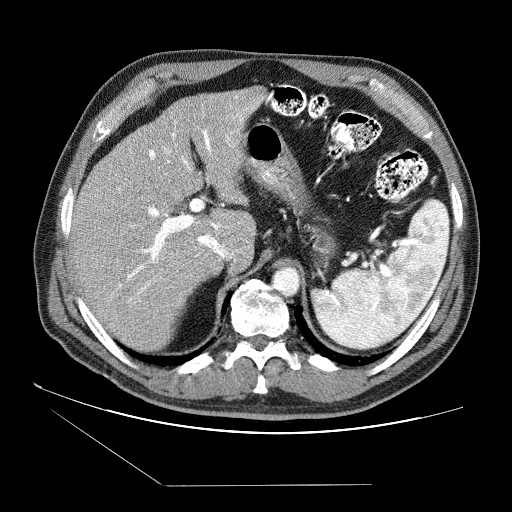
Contrast-enhanced abdominal CT (liver protocol), one axial slice. Slice 54 of 87 in the series (ordered by position). Reconstruction kernel STANDARD. Soft-tissue window (W 400 / L 40 HU). 2.5 mm slice thickness. 512 × 512 image matrix, field of view 400 × 400 mm. From the clinical record (not read from this slice): diagnosis: hepatocellular carcinoma (patient treated with transarterial chemoembolisation; whether this scan precedes or follows treatment is not stated here); TNM stage (as recorded): Stage-II; Child-Pugh class: B; tumour nodularity: multinodular; tumour size: 2.6 cm.
Structures marked on this image (semi-automatically segmented with operator editing):
- liver parenchyma outside the tumour (the mass and vessels are separate outlines, so this box may not span the whole liver): bounding box <70,88,264,350> (left, top, right, bottom; pixels)
- liver vessels: <78,95,254,307>